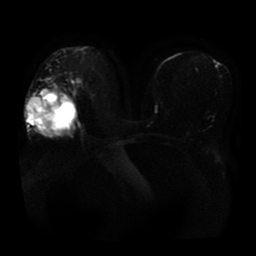
Breast MRI, one axial slice; slice 25 of 41 in the series (ordered by position); diffusion-weighted series; image 2 of 4 stored at this slice position (different b-values; order by instance number); 1.5 T; 5 mm slice thickness; 256 × 256 image matrix, field of view 360 × 360 mm. Female patient.
Structures marked on this image (manually delineated by an expert):
- tumour on diffusion-weighted imaging: bounding box <27,97,76,140> (left, top, right, bottom; pixels)